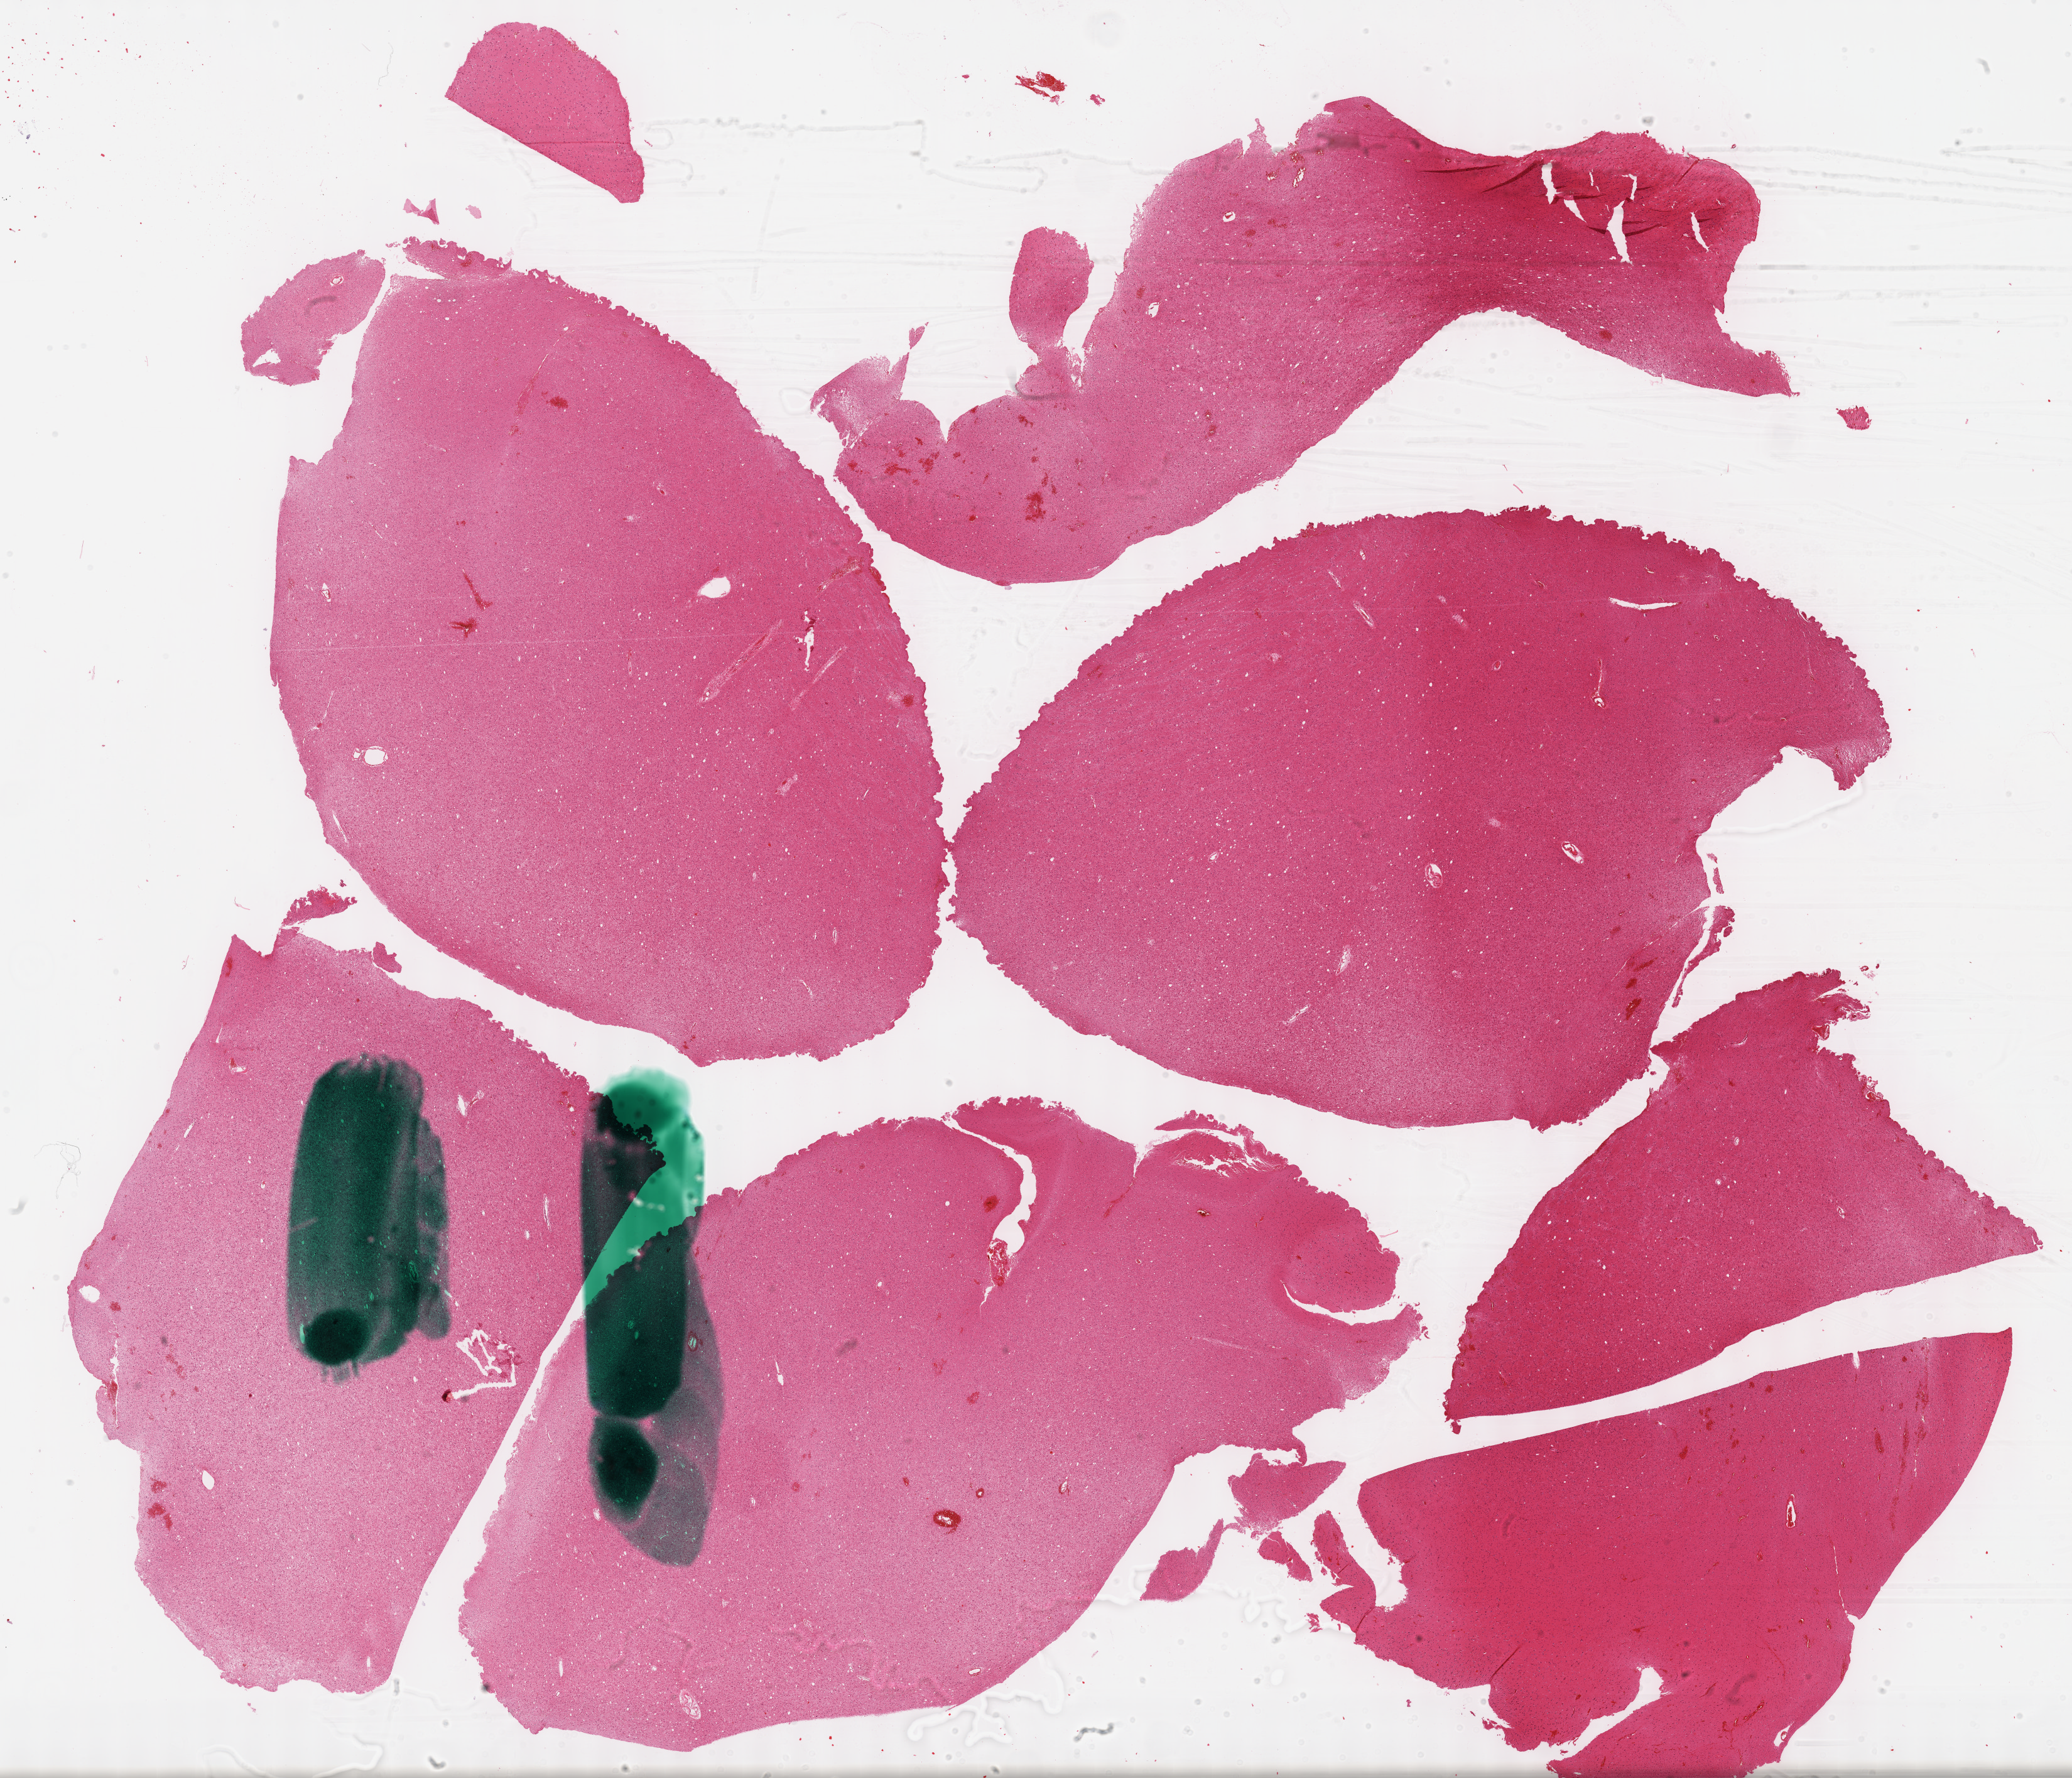
Digitized H&E-stained tissue section (whole slide) — whole scanned area (about 26.7 x 22.9 mm, slide scanned at 40x) shown as a low-resolution overview. Formalin-fixed paraffin-embedded (FFPE) diagnostic section. Sample: primary tumour, brain. Female, age 22 years at initial diagnosis. Histologic grade: G3 (poorly differentiated).
- diagnosis: Astrocytoma, anaplastic (cerebrum)
- laterality: right